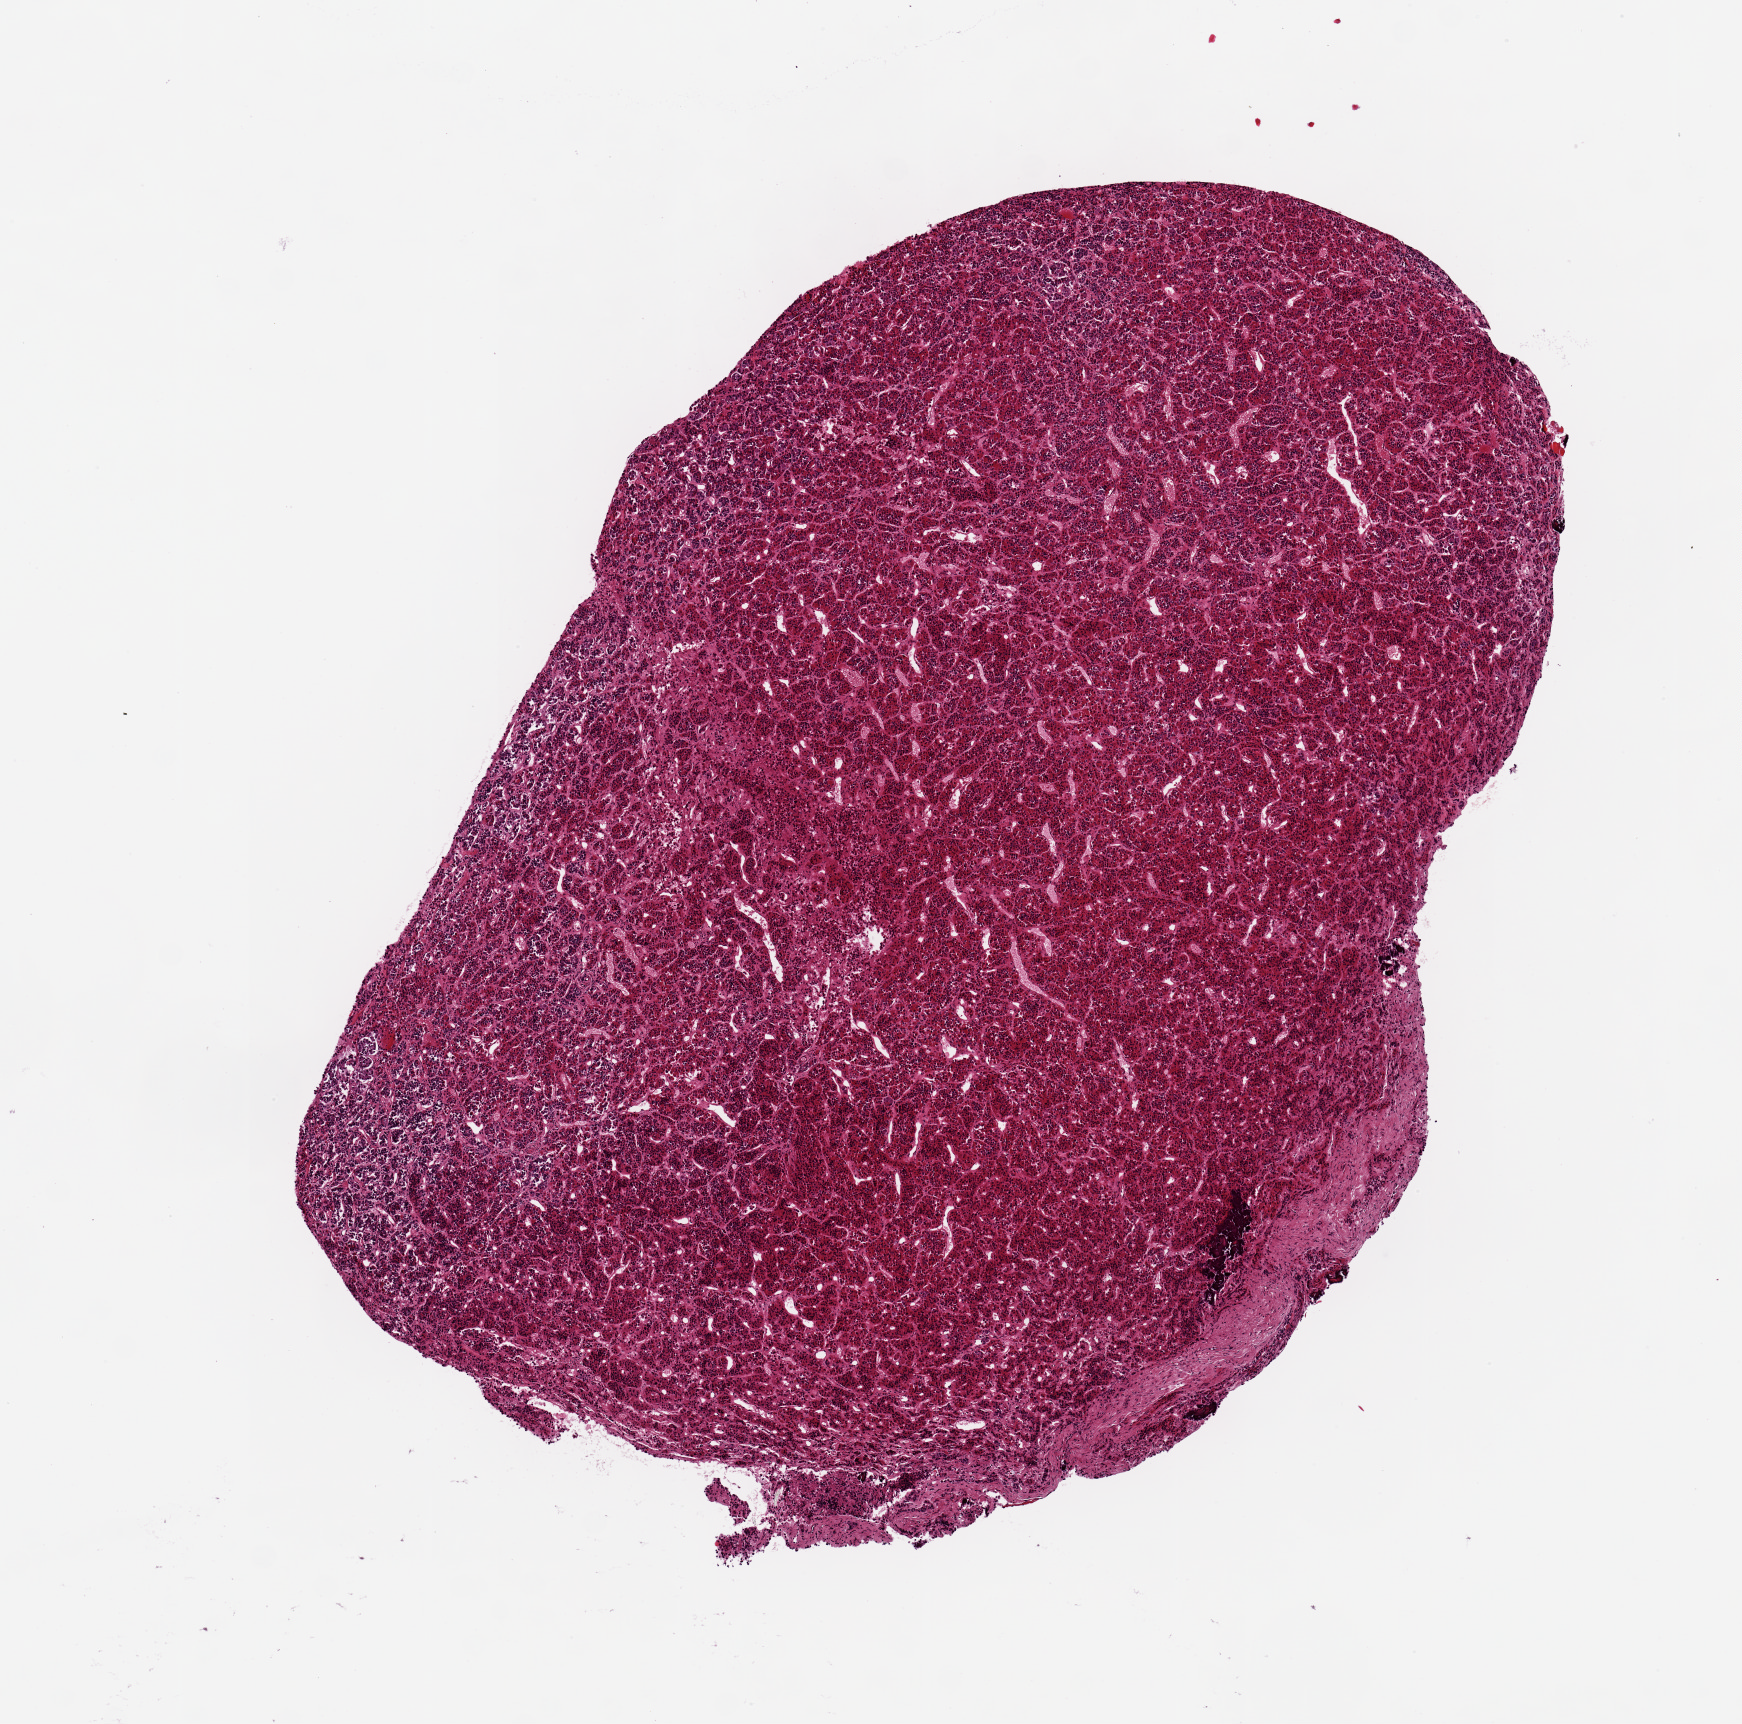
Digitized haematoxylin and eosin-stained section, brightfield — whole scanned area (about 6.9 x 6.8 mm, slide scanned at 20x) shown as a low-resolution overview, PAXgene-fixed paraffin-embedded (PFPE) section, sampled site (target tissue): pituitary, tissue donor sample. Female donor.
Pathologist's review note for this sample: 1 ~ 6x4mm aliquot.